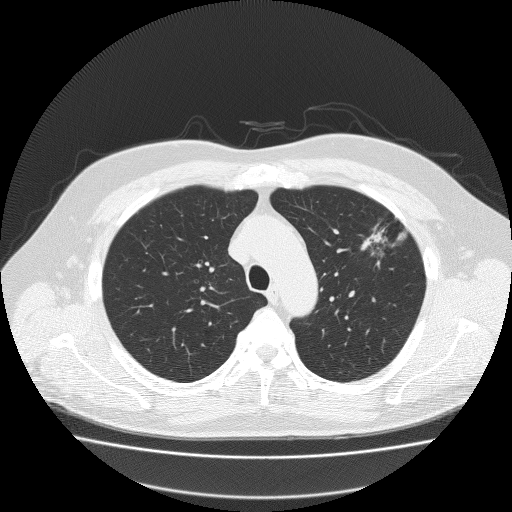
Low-dose screening chest CT, axial slice; baseline annual screen; lung window (W 1500 / L -600 HU); lung (sharp) reconstruction kernel (FC51). Male participant, aged 62 years at enrolment. Former smoker at enrolment.
Expert-annotated lung lesion, bounding box <352,208,420,264> (left, top, right, bottom; pixels). Screening reader's record for this exam (one nodule recorded; not confirmed to be the boxed lesion): non-calcified nodule or mass ≥4 mm, left upper lobe, 18 × 8 mm, spiculated (stellate) margins, soft tissue attenuation. Official screen result: positive, change unspecified: nodule(s) >= 4 mm or enlarging nodule(s), mass(es), or other non-specific abnormalities suspicious for lung cancer.